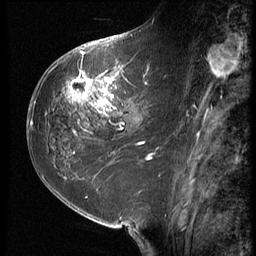
Breast MRI (dynamic contrast-enhanced), one sagittal slice; 3 images stored at this slice position (order not interpretable as contrast timing); 1.5 T; TE 4.2 ms, TR 9 ms; 2.5 mm slice thickness; 256 × 256 image matrix, field of view 180 × 180 mm. Patient: female, 59 years. Case-level facts recorded for this patient, not image findings: setting: breast cancer imaged before/during neoadjuvant chemotherapy; receptor status: HER2-positive.
Structures marked on this image (semi-automatic segmentation, software-assisted and operator-edited):
- analysis volume of interest (the breast-tissue region the enhancement analysis was run in; not a lesion): box from (x=54, y=65) to (x=155, y=132) px
- tumour enhancement mask (voxels above the 140 % enhancement threshold inside the analysis volume of interest): (x=63, y=65)–(x=148, y=127)